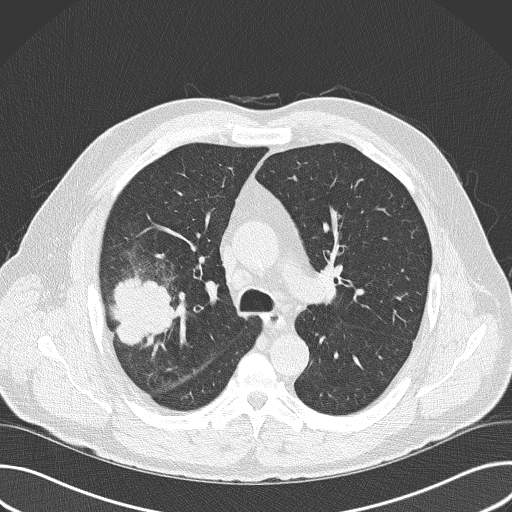
Chest CT (low-dose screening protocol), one axial image. Baseline annual screen. Lung window (W 1500 / L -600 HU). 2 mm slice thickness. Lung (sharp) reconstruction kernel (B50f). 120 kVp. 512 × 512 image matrix, field of view 380 × 380 mm. Male participant, aged 56 years at enrolment. Current smoker at enrolment.
Expert reader's lesion annotation, bounding box (x1, y1, x2, y2) in pixels: (82, 264, 187, 372). Screening reader's record for this exam (one nodule recorded; not confirmed to be the boxed lesion): non-calcified nodule or mass ≥4 mm, right upper lobe, 6 × 5 mm, spiculated (stellate) margins, soft tissue attenuation. Official screen result: positive, change unspecified: nodule(s) >= 4 mm or enlarging nodule(s), mass(es), or other non-specific abnormalities suspicious for lung cancer. Later outcome: lung cancer diagnosed 16 days after this screen — adenocarcinoma, NOS, right upper lobe, poorly differentiated (G3), stage IIB (AJCC 6th edition), 60 mm at pathology.